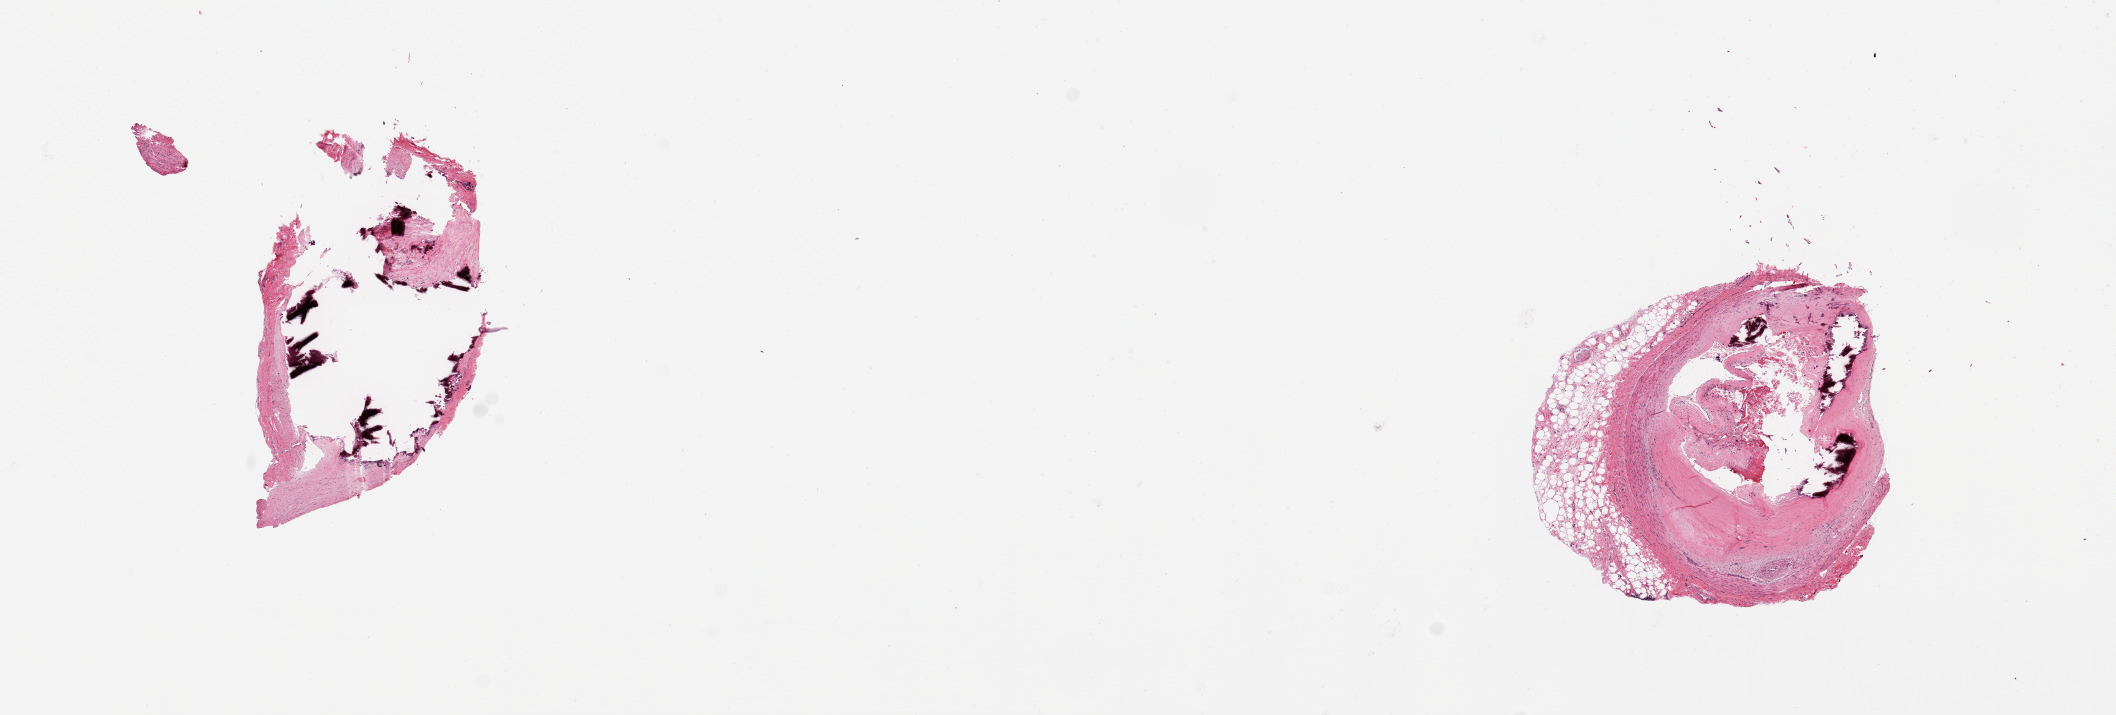
Hematoxylin and eosin (H&E) whole-slide image — whole scanned area (about 16.7 x 5.7 mm) shown as a low-resolution overview; PAXgene-fixed paraffin-embedded (PFPE) section; section of coronary artery (target tissue); donor tissue sample. Donor sex: female.
Reviewer comment on this tissue sample: 2 pieces, 3x2 & 3x3mm; Subtotally occlusive calcified atherosclerosis.